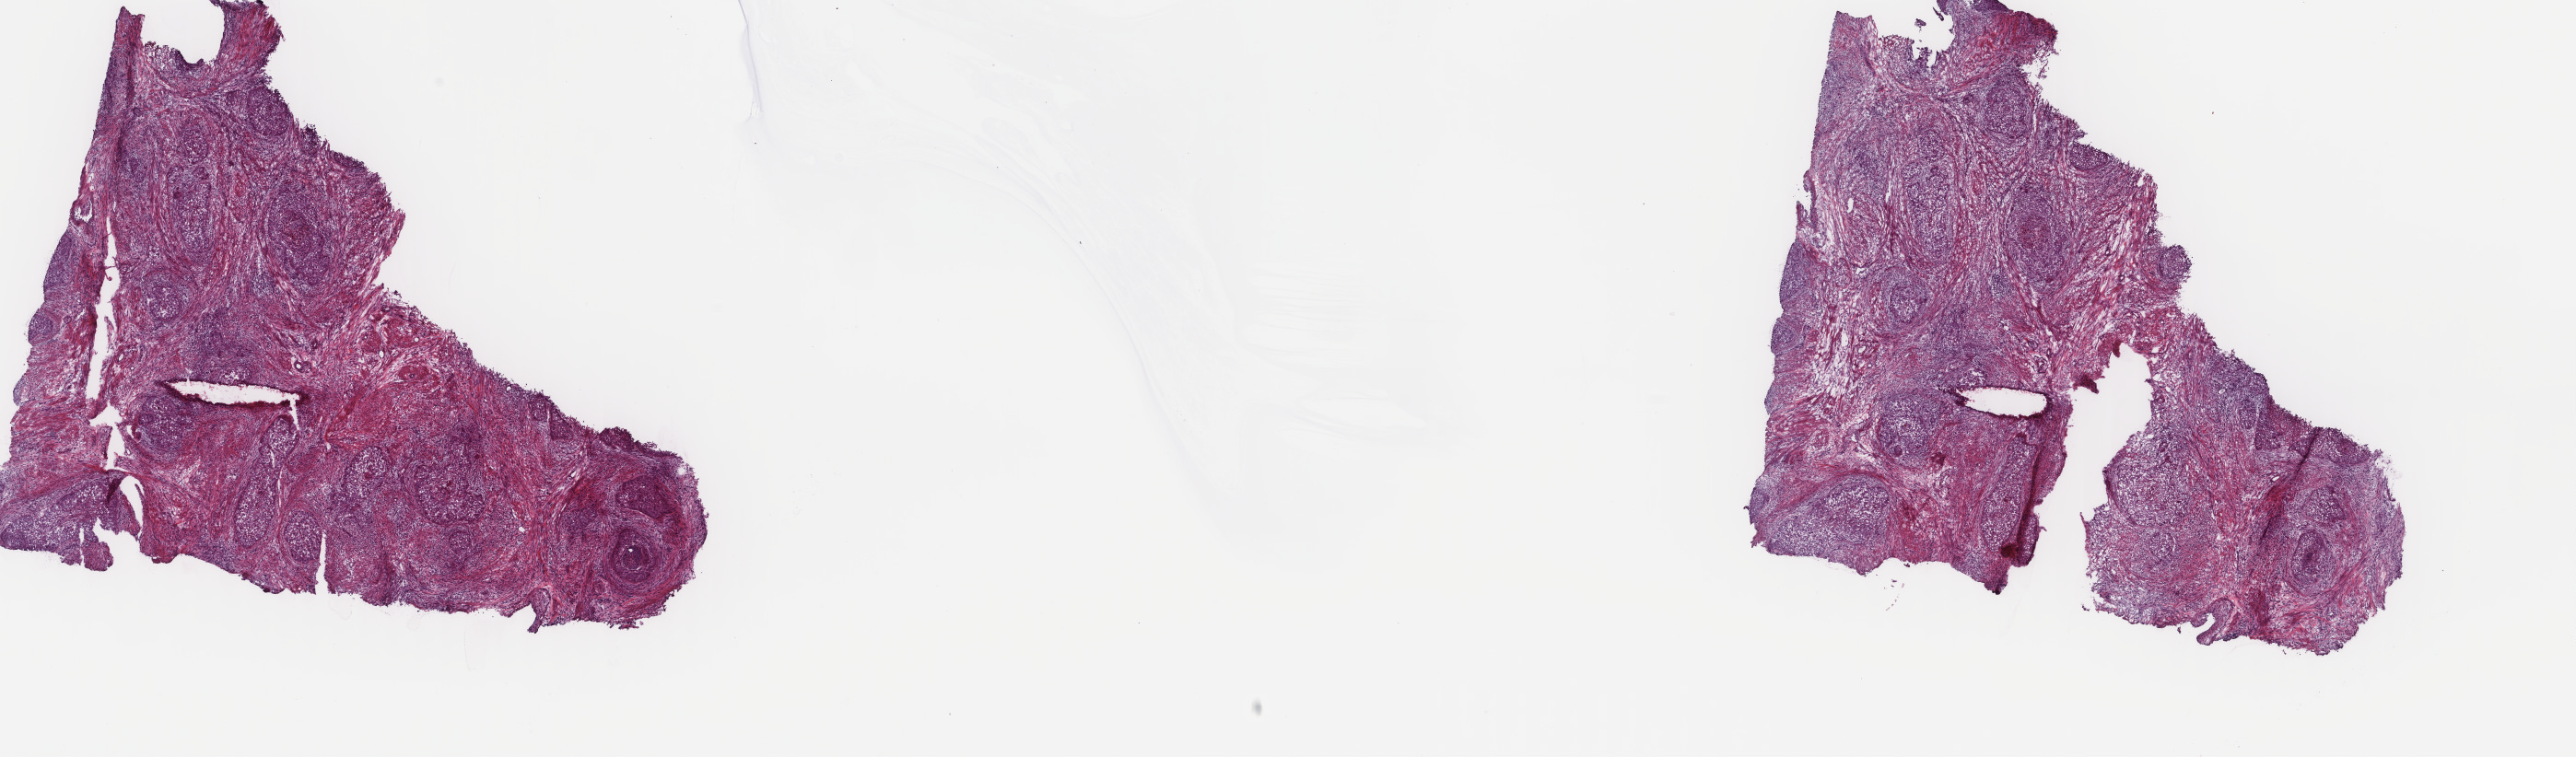
H&E-stained whole-slide image — low-resolution overview of the scanned area, about 22.2 x 6.5 mm; frozen section from the top of the tissue portion; sample: primary tumour, cervix. Female, age 46 years at initial diagnosis. Histologic grade: G2 (moderately differentiated). Composition of this section per pathologist review: tumour cells 60%, tumour nuclei 60%, normal cells 10%, stromal cells 20%, necrosis 10%. Infiltration values recorded for this section: lymphocyte infiltration 60%, monocyte infiltration 10%, neutrophil infiltration 20%.
Pathologic diagnosis: Squamous cell carcinoma, large cell, nonkeratinizing, NOS (cervix uteri). Lymph nodes positive (case pathology): 0 of 18 examined. FIGO stage: IB1.